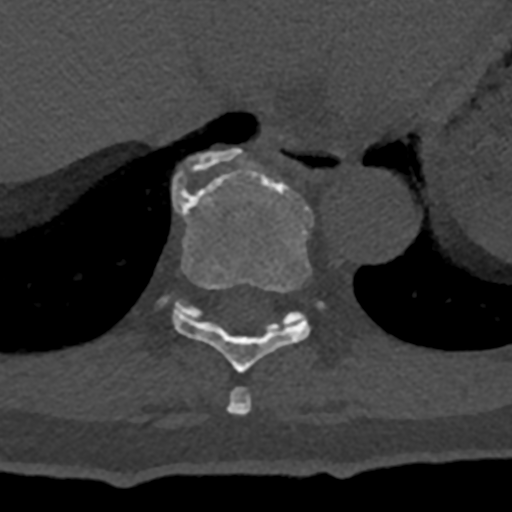
CT including the spine, one axial slice; slice 643 of 797 in the series (ordered by position); reconstruction kernel Br40s/3; 120 kVp; bone window (W 1800 / L 400 HU); 0.5 mm slice thickness; 512 × 512 image matrix. Patient: male, 74 years. From the clinical record (not read from this slice): primary cancer: renal; vertebrae with lytic lesions (as recorded): T10, L1, L2, L3, L4, L5.
Structures marked on this image (semi-automatic segmentation, software-assisted and operator-edited):
- T10 vertebra: bounding box <157,148,325,328> (left, top, right, bottom; pixels)
- T8 vertebra: <228,388,252,415>
- T9 vertebra: <172,171,313,373>